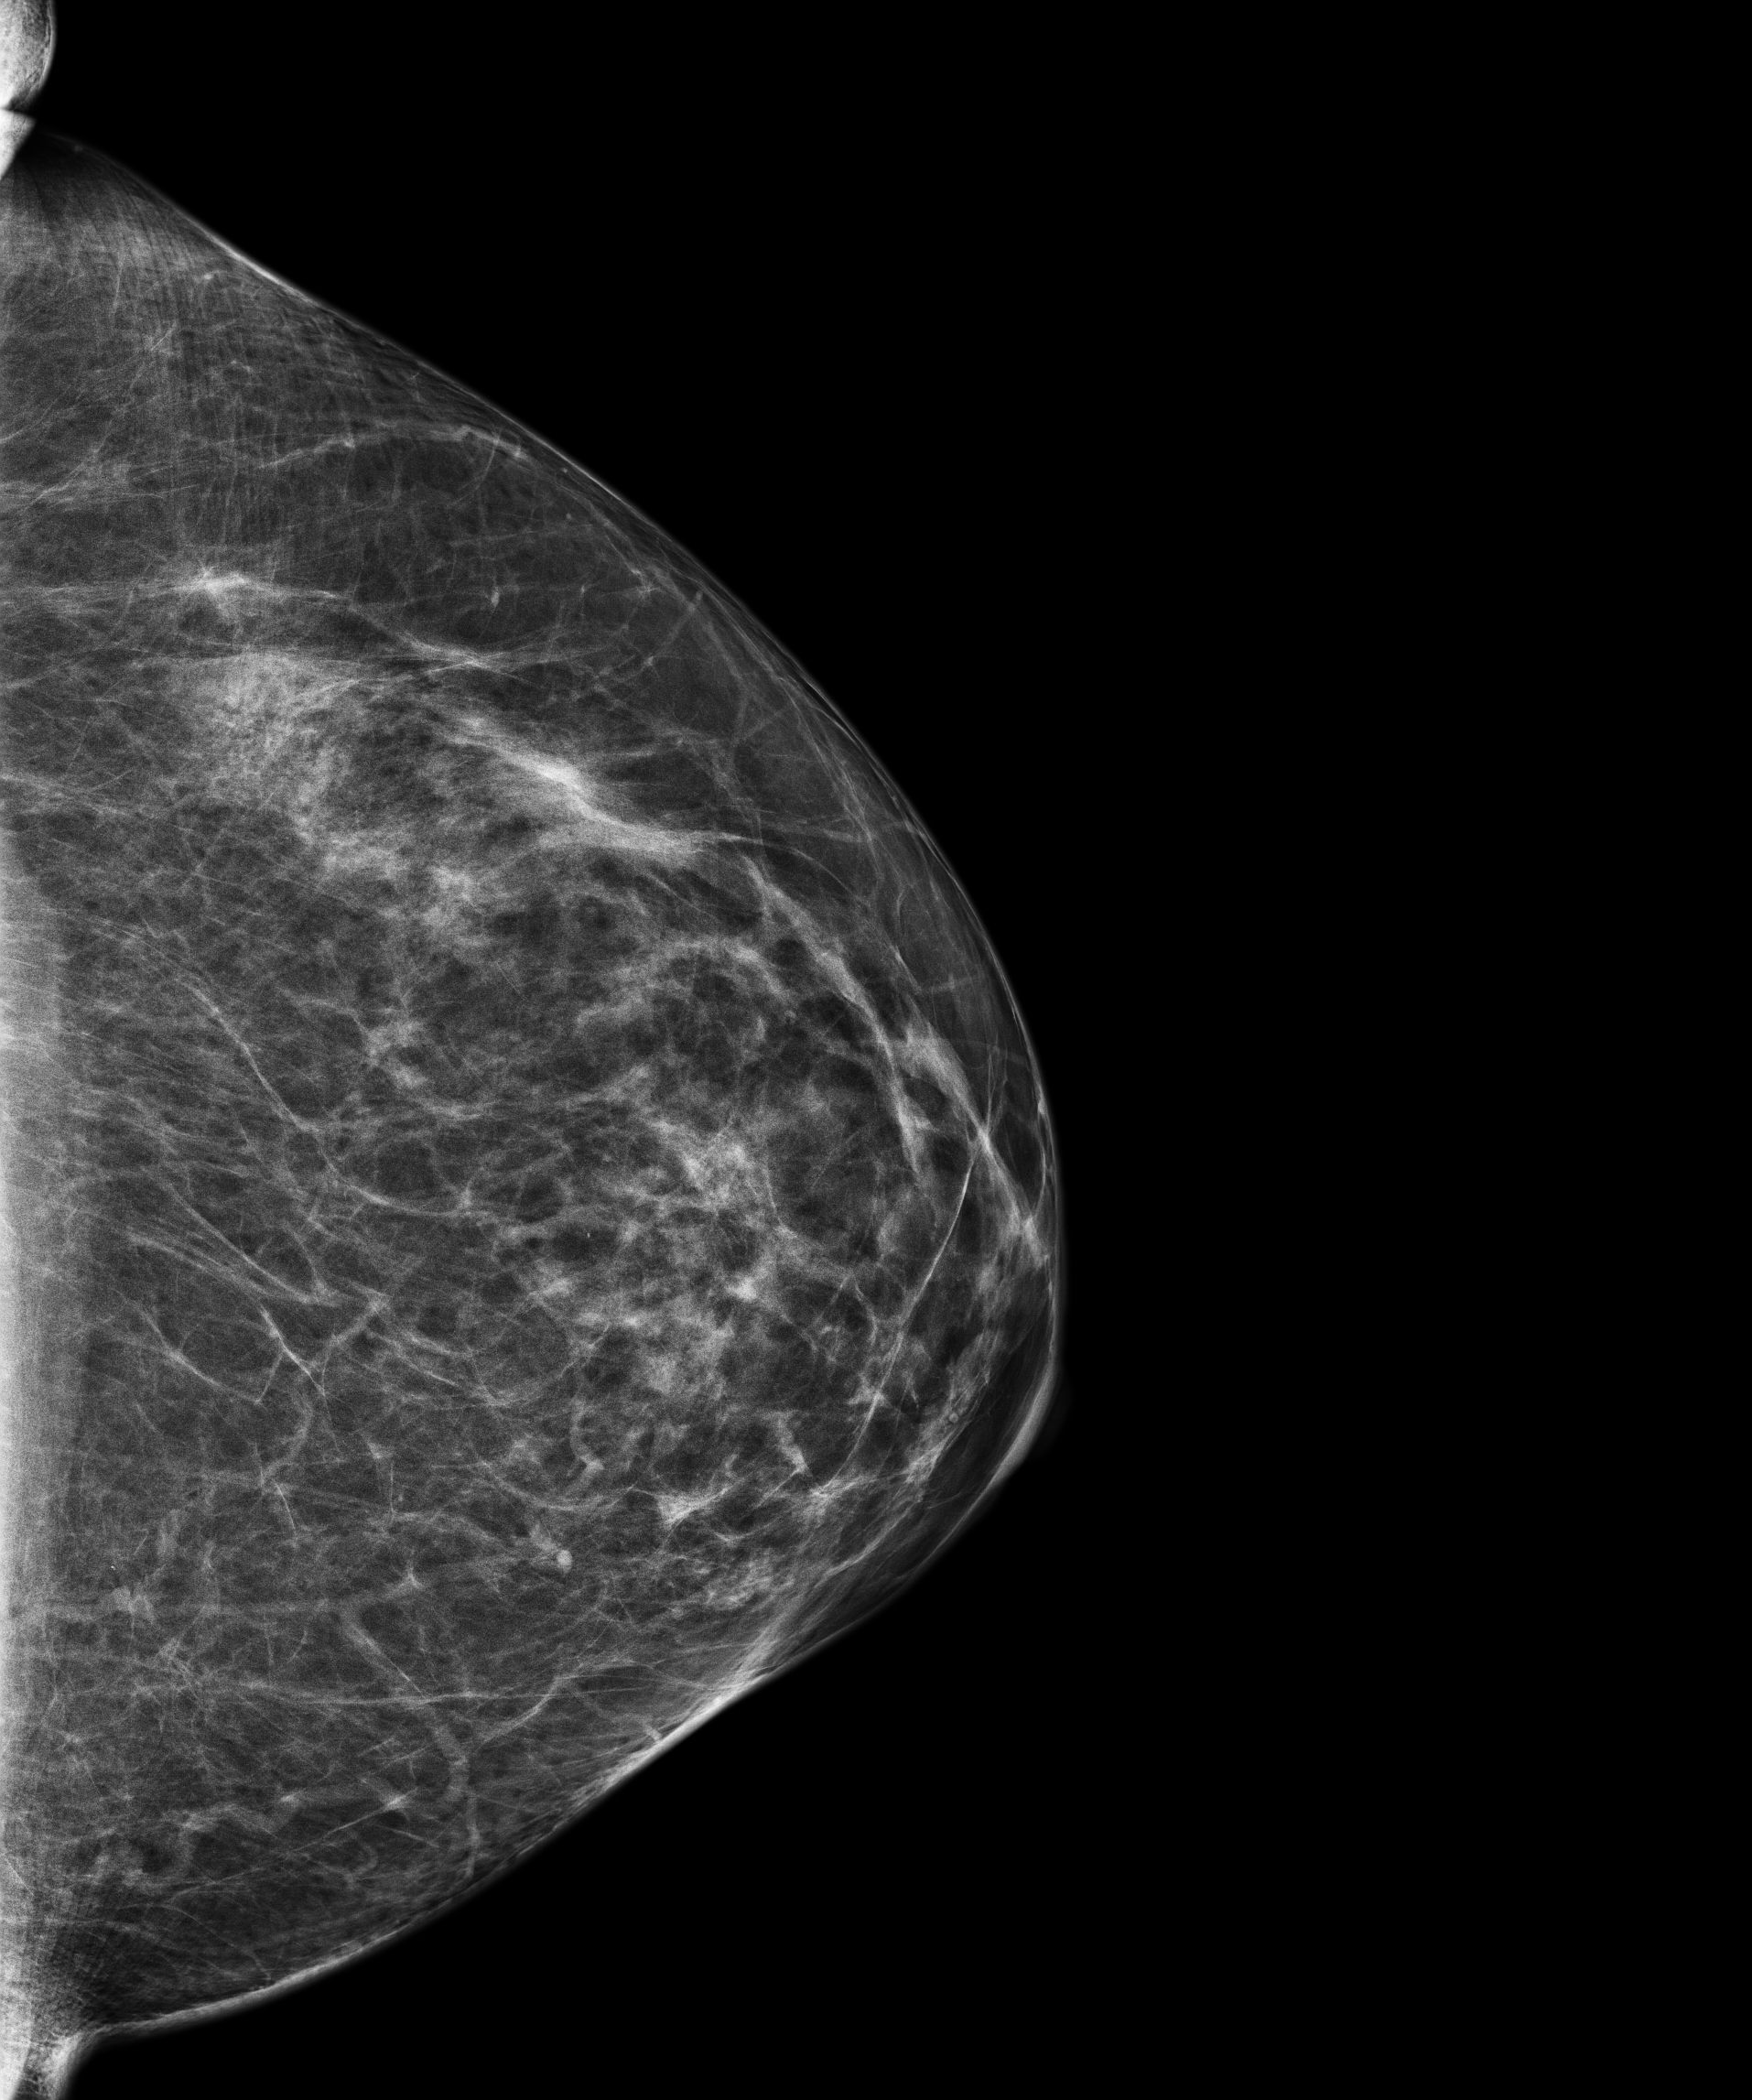
Annual screening mammography examination; system: Senographe Pristina. Female patient, age 58 years.
Image type: full-field digital mammogram. Breast: left. Projection: CC view.